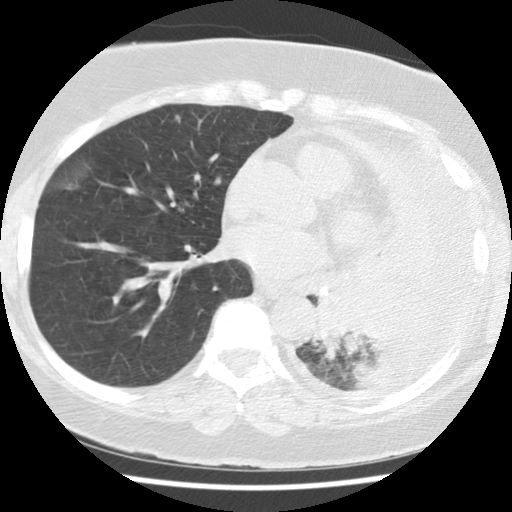
Chest CT (low-dose screening protocol), one axial image; baseline annual screen; lung window (W 1500 / L -600 HU); 512 × 512 image matrix, field of view 320 × 320 mm. Female participant, aged 65 years at enrolment. Current smoker at enrolment.
- Expert-annotated lung lesion, bounding box [x1, y1, x2, y2] px = [307, 282, 420, 375].
- Screening reader's record for this exam (one nodule recorded; not confirmed to be the boxed lesion): non-calcified nodule or mass ≥4 mm, left lower lobe, 74 × 48 mm, spiculated (stellate) margins, soft tissue attenuation.
- Lung cancer was diagnosed 13 days after this screen: adenocarcinoma, NOS, left lower lobe, stage IV (AJCC 6th edition), 74 mm at pathology.